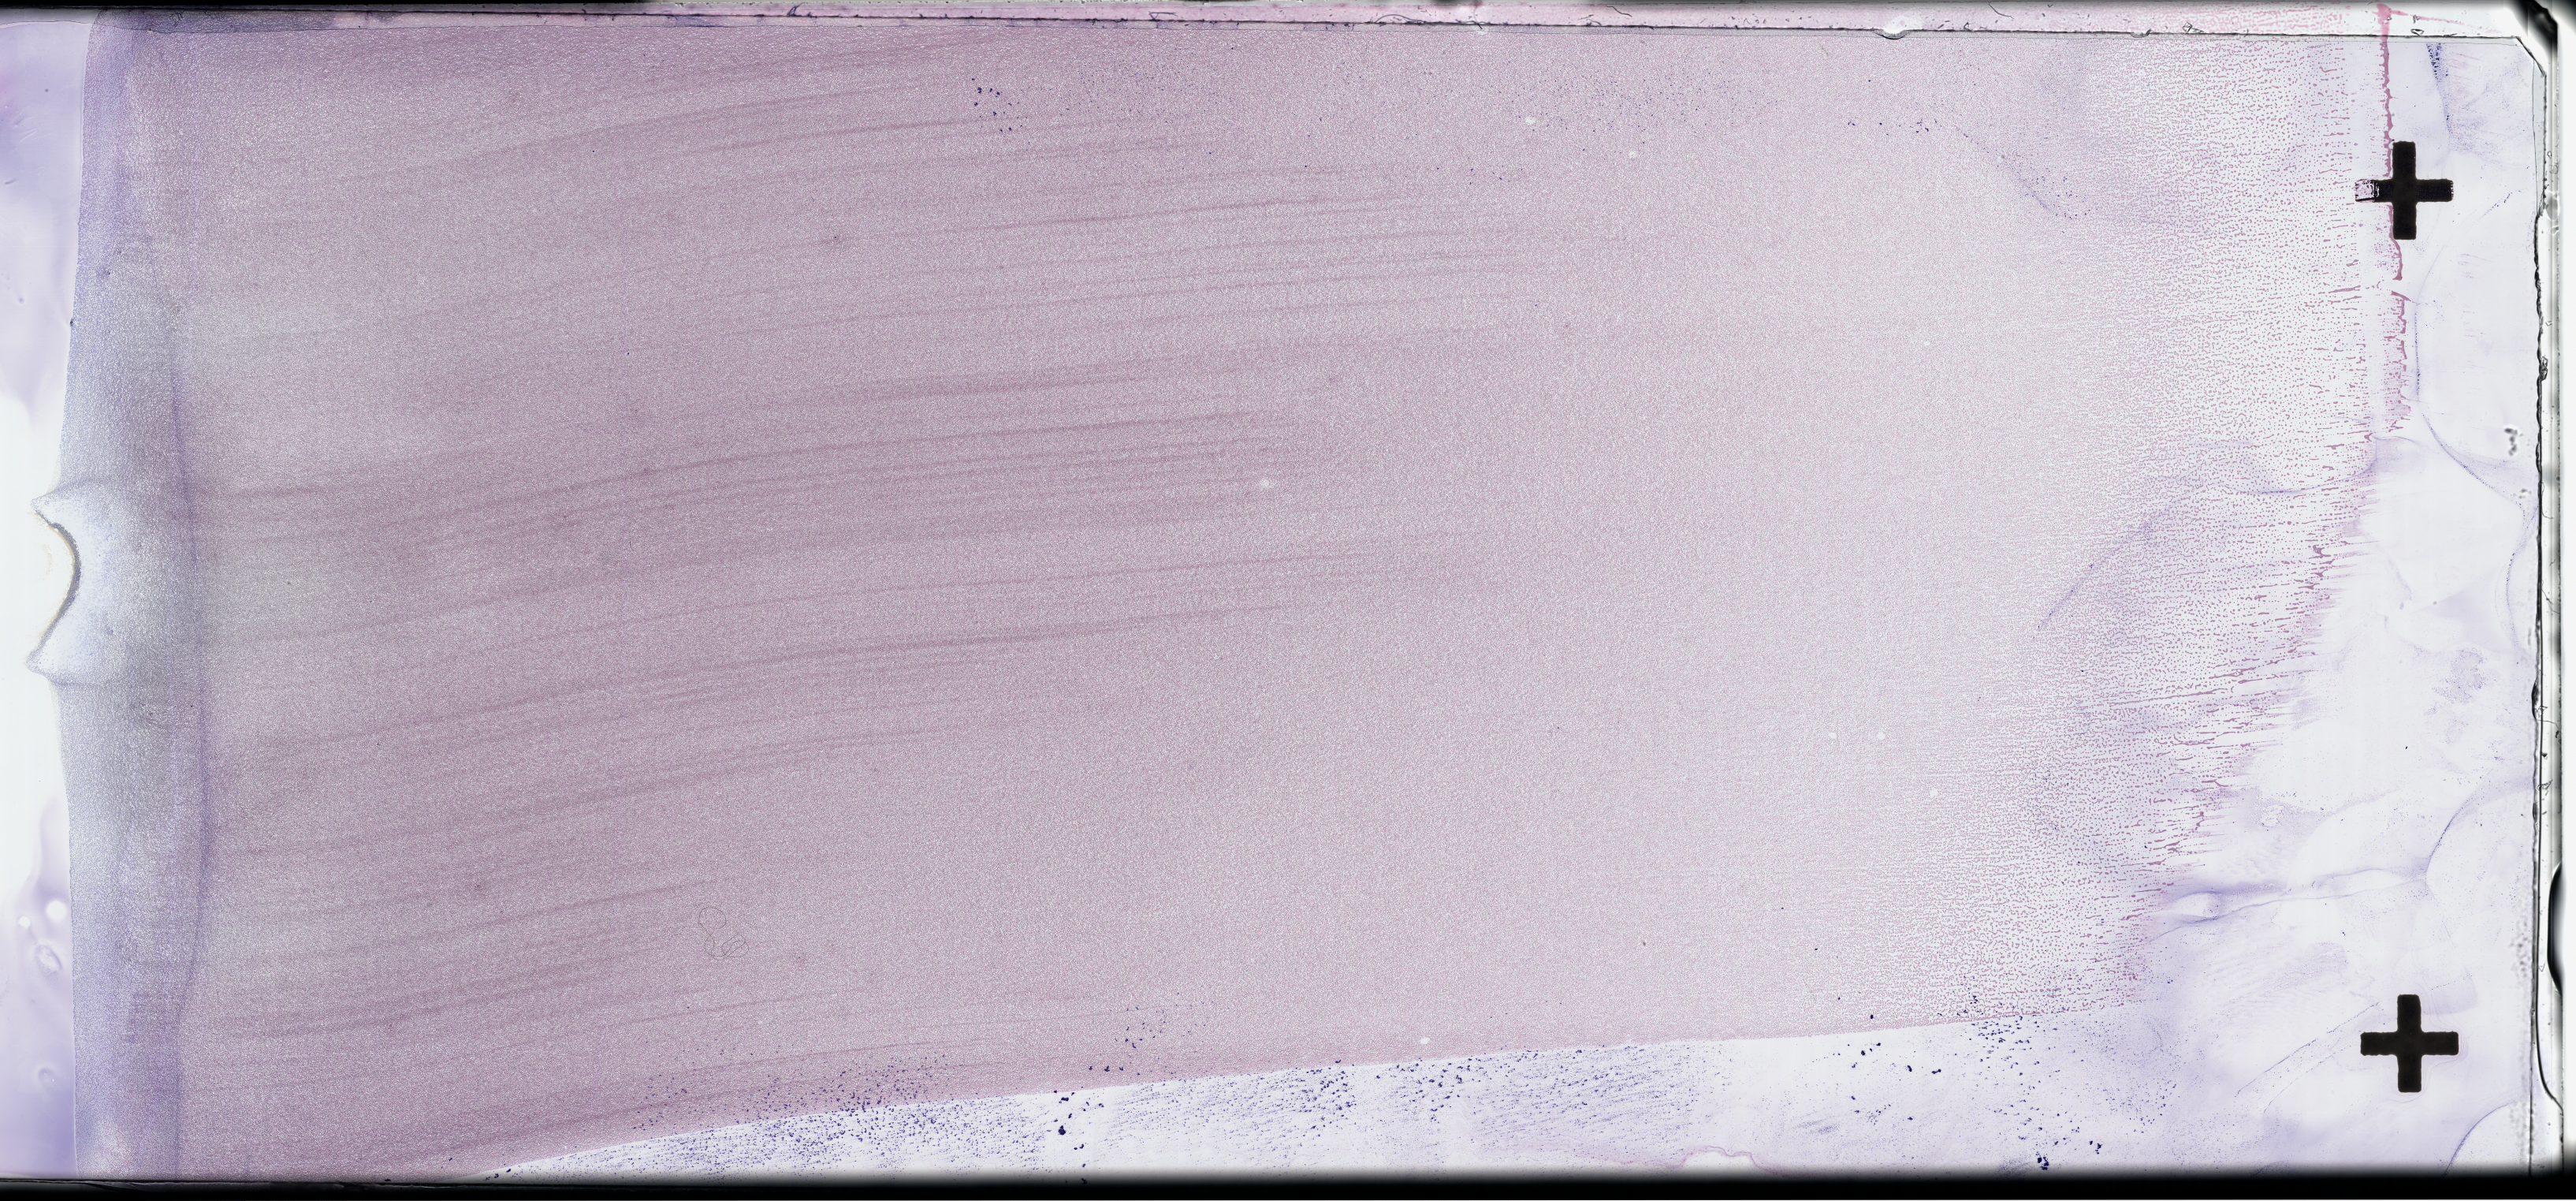
Wright-Giemsa-stained bone marrow smear, whole-slide image — low-resolution overview of the scanned area, about 52.8 x 24.6 mm; EDTA-anticoagulated smear; specimen time point: collected on treatment. Male patient.
From a patient with: Acute Myeloid Leukemia Not Otherwise Specified.